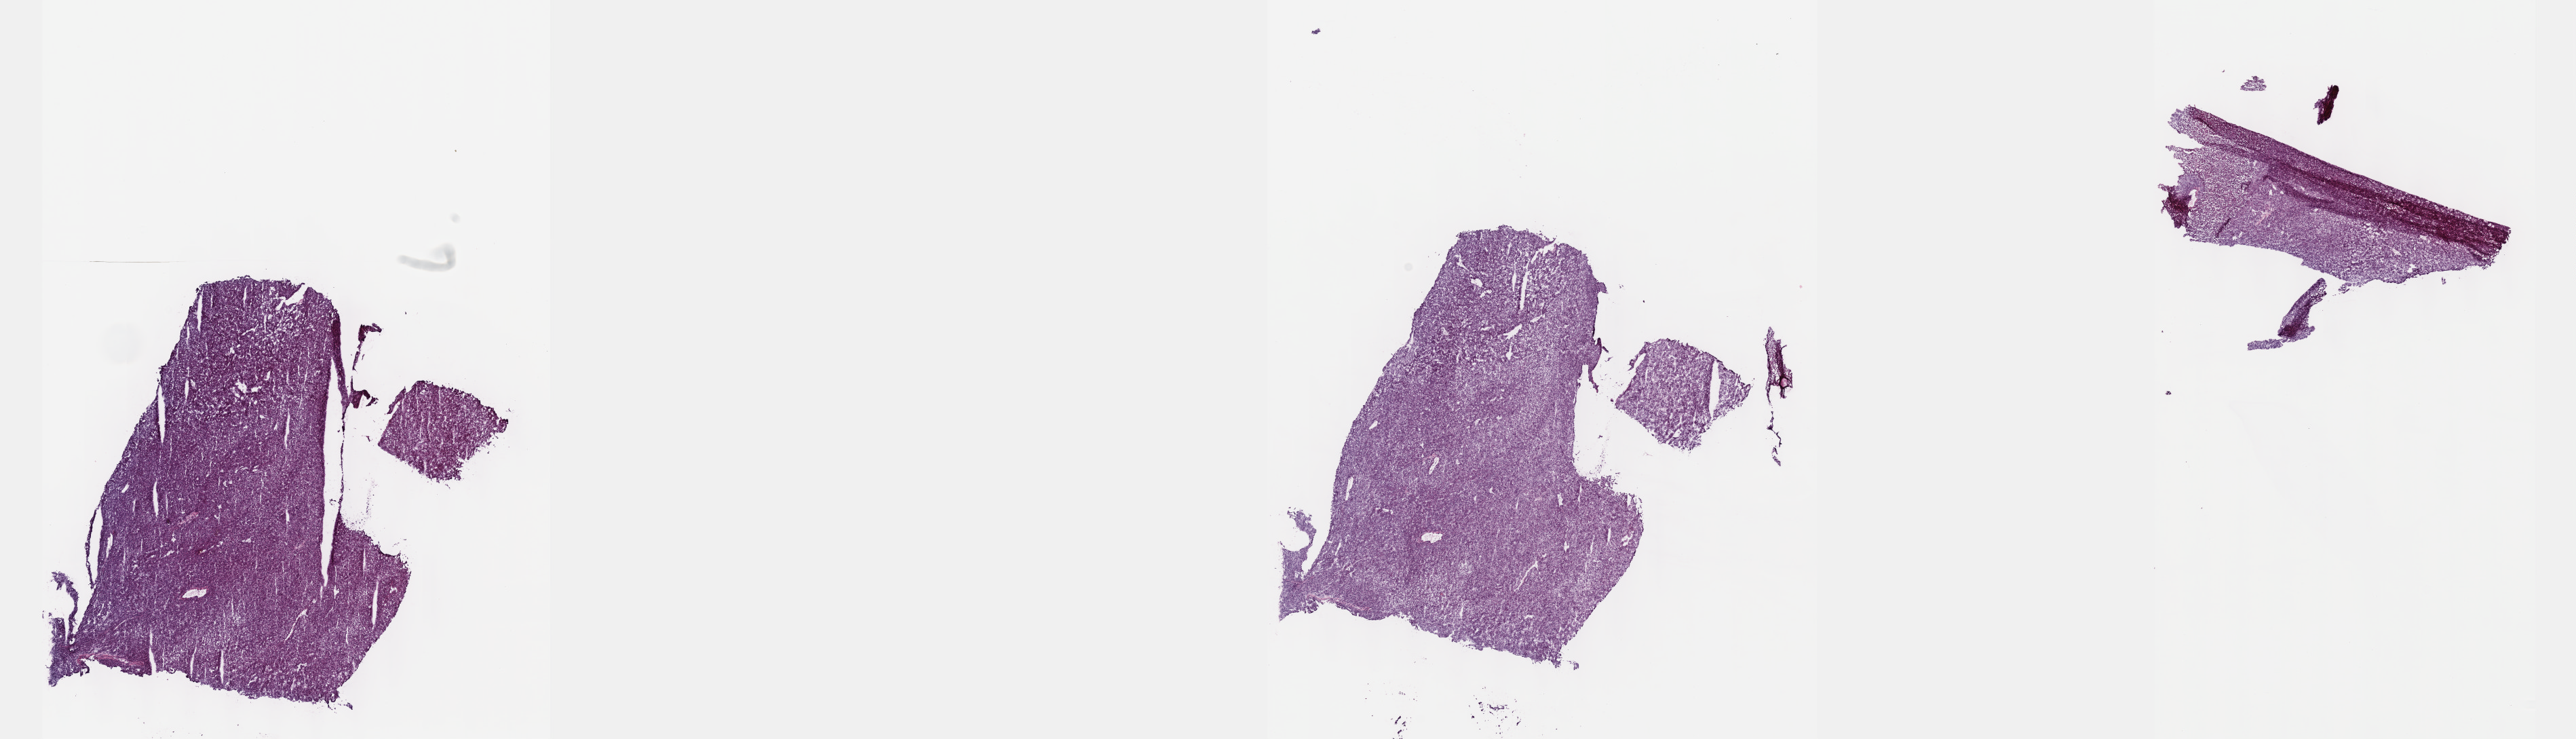
H&E-stained whole-slide image — whole scanned area (about 30.7 x 8.8 mm, from a 40x scan) shown as a low-resolution overview. Frozen section. Sample: primary tumour, liver. Patient: male, age at initial diagnosis 58 years. Slide review estimates, as recorded: tumour cells 100%, tumour nuclei 80%.
Diagnosis: Hepatocellular carcinoma, NOS.